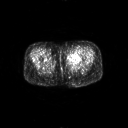
FDG PET of an extremity soft-tissue mass (from a PET/CT study), one axial slice; 128 × 128 image matrix, field of view 700 × 700 mm. Patient: female, 47 years. From the clinical record (not read from this slice): histological type: myxofibrosarcoma; grade: intermediate; site of the primary tumour: left thigh.
Annotated regions visible in this slice (expert contour drawn on MRI and transferred to this co-registered scan by the dataset authors):
- gross tumour volume including surrounding oedema: box from (x=67, y=54) to (x=82, y=62) px
- gross tumour volume (mass): (x=74, y=54)–(x=79, y=56)